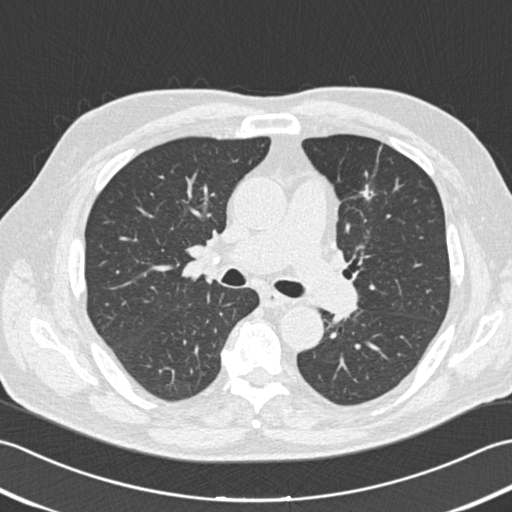
Axial slice from a low-dose chest CT screening exam; second screening round (one year after baseline); lung window (W 1500 / L -600 HU). Male participant, aged 74 years at enrolment. Former smoker at enrolment.
• Expert-annotated lung lesion, bounding box (x1, y1, x2, y2) in pixels: (346, 172, 392, 216).
• The screening reader recorded 5 non-calcified nodules or masses ≥4 mm on this exam (left upper lobe, right upper lobe, left lower lobe, left lower lobe, left lower lobe); which of them this box marks is not recorded.
• Official screen result: positive, other.